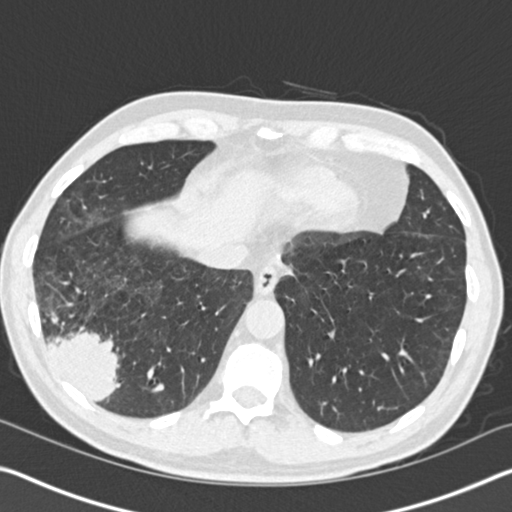
Low-dose screening chest CT, axial slice. Baseline screening round. Lung window (W 1500 / L -600 HU). 2 mm slice thickness. 120 kVp. 512 × 512 image matrix, field of view 340 × 340 mm. Male participant, aged 61 years at enrolment.
Lesion marked by an expert reader, box from (x=18, y=286) to (x=141, y=416) px. Reader record for this screening exam (exam-level; its link to the box is not recorded): non-calcified nodule or mass ≥4 mm, right lower lobe, 52 × 36 mm, spiculated (stellate) margins, soft tissue attenuation. Later outcome: lung cancer diagnosed 392 days after this screen — bronchiolo-alveolar adenocarcinoma, NOS, right lower lobe, moderately differentiated (G2), stage IIIB (AJCC 6th edition), 90 mm at pathology.